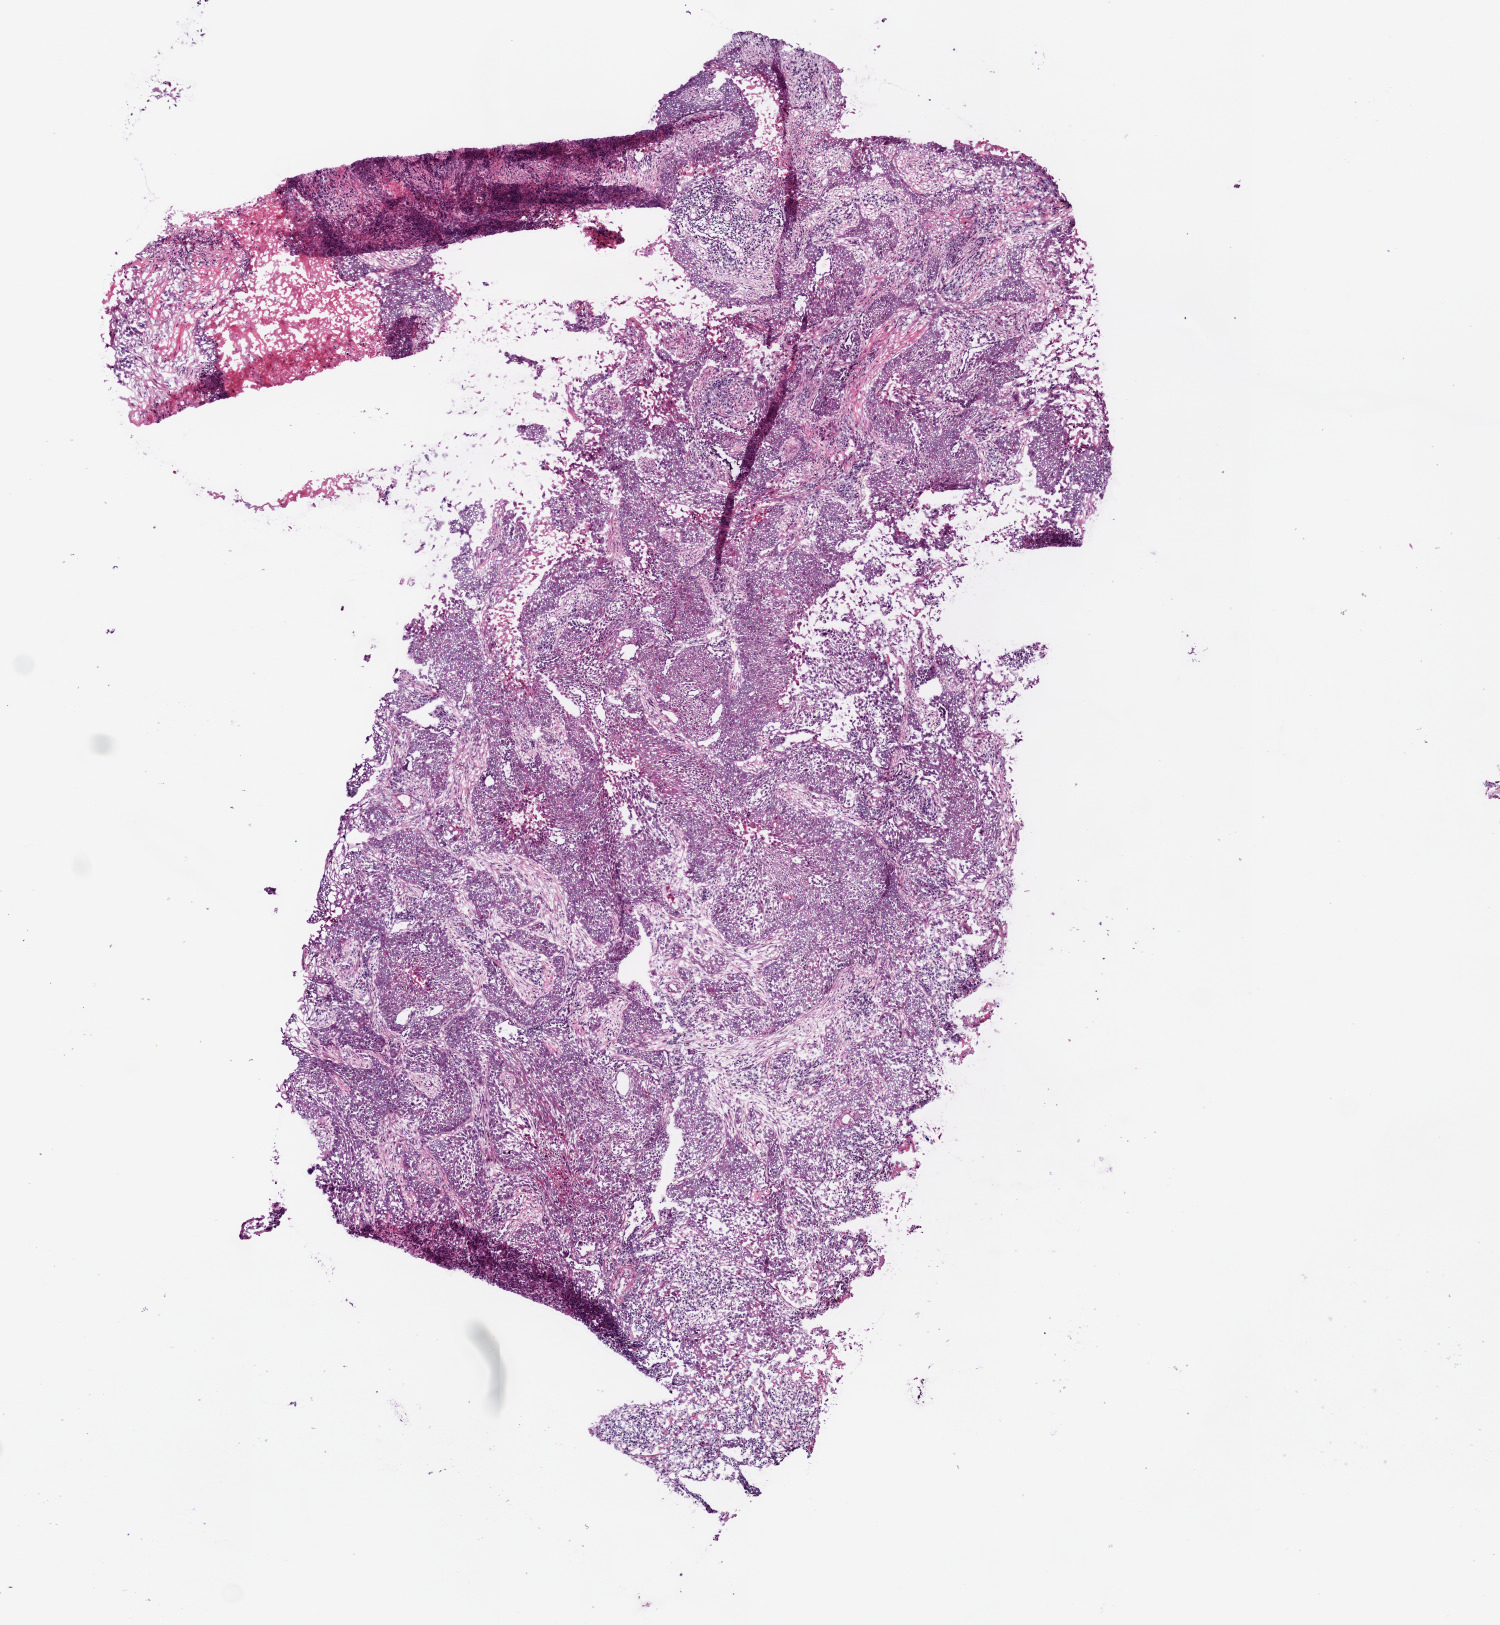
H&E-stained whole-slide image, whole scanned area (about 6.0 x 6.5 mm) shown as a low-resolution overview; frozen section; lung, primary tumour sample. Female, age 73 years at initial diagnosis. Slide review estimates, as recorded: tumour cells 85%, tumour nuclei 80%.
Histologic diagnosis: Squamous cell carcinoma, NOS.